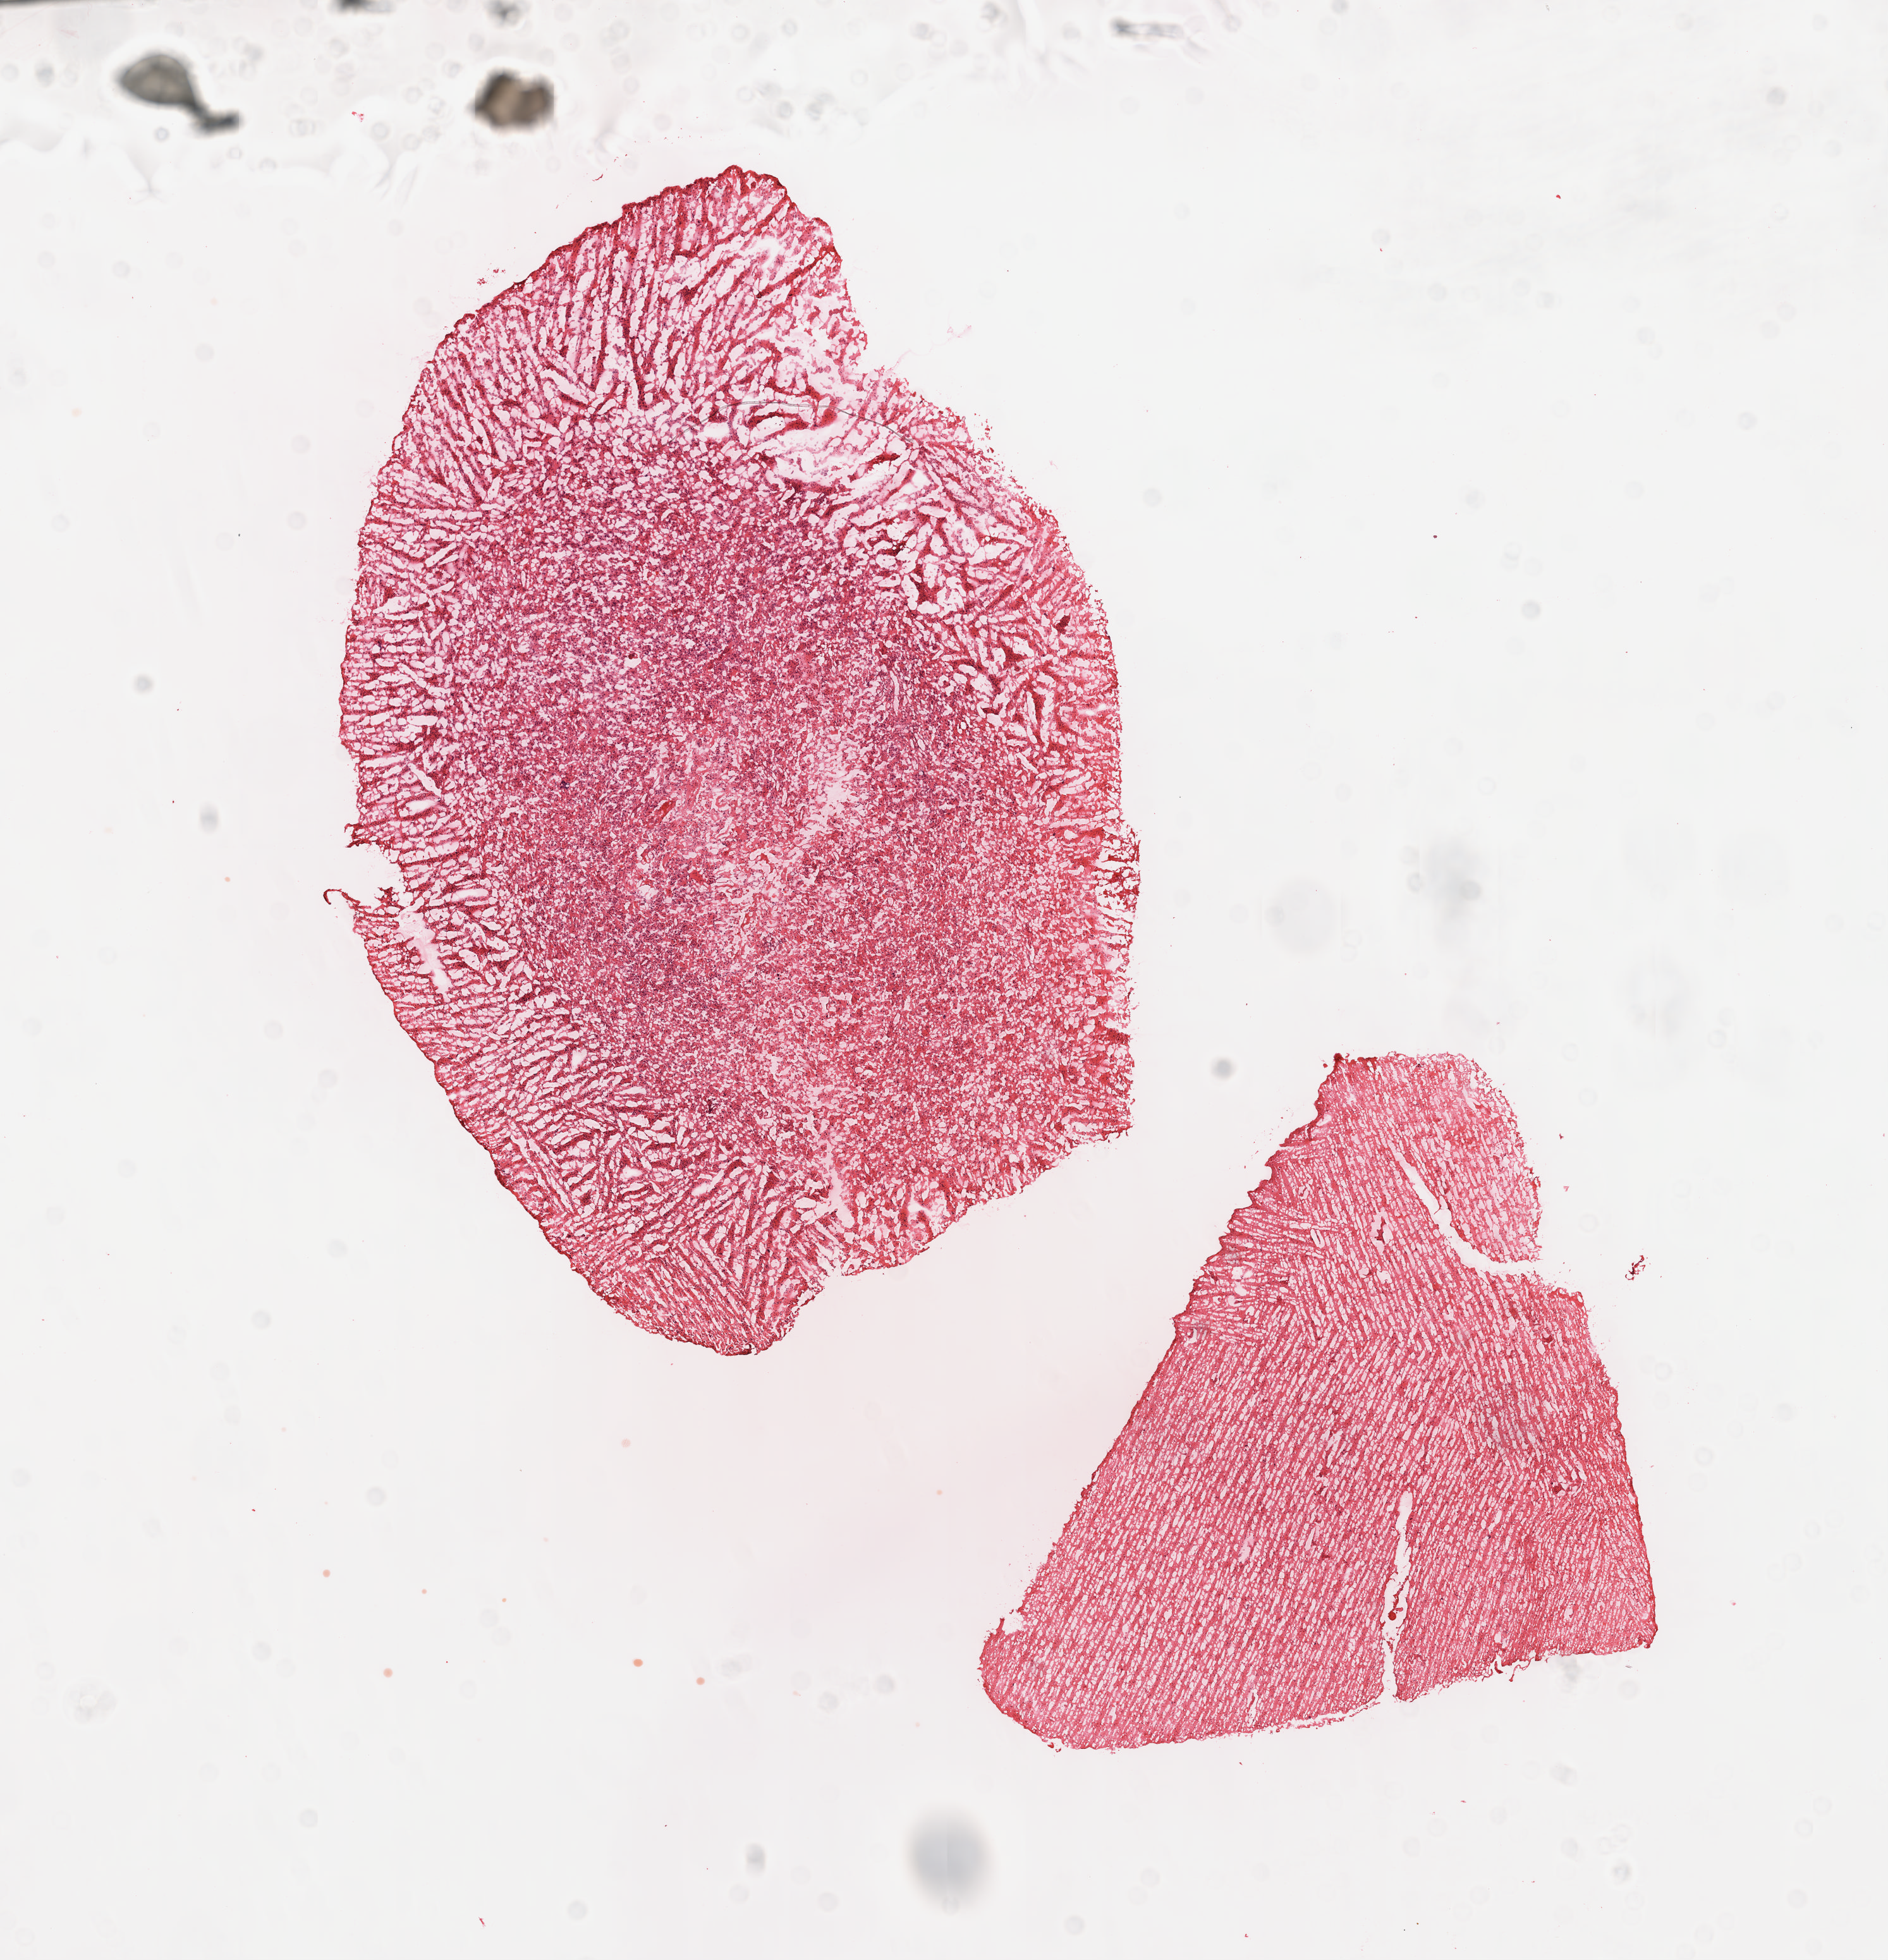
Digitized H&E-stained tissue section (whole slide), shown as a low-resolution overview of the whole scanned area (about 12.1 x 12.5 mm), frozen section from the top of the tissue portion, brain, primary tumour sample. Female, age 38 years at initial diagnosis.
Histologic diagnosis: Glioblastoma.